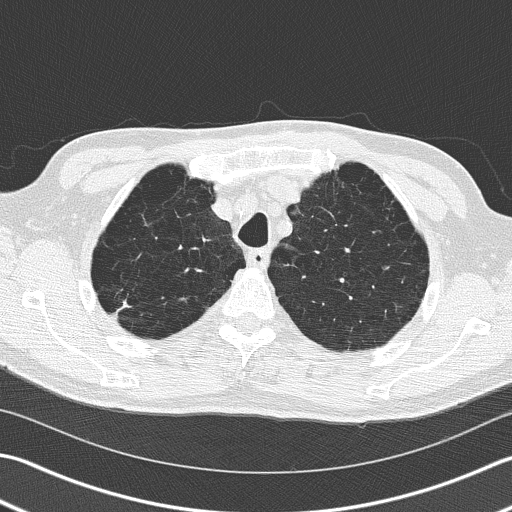
Low-dose screening chest CT, one axial slice; slice 130 of 163 in the series (ordered by position); lung window (W 1500 / L -600 HU); 2 mm slice thickness; 512 × 512 image matrix.
Annotated regions visible in this slice (outlined manually by an expert reader):
- lesion 1 (tumor, upper lobe of right lung): box from (x=122, y=302) to (x=128, y=308) px